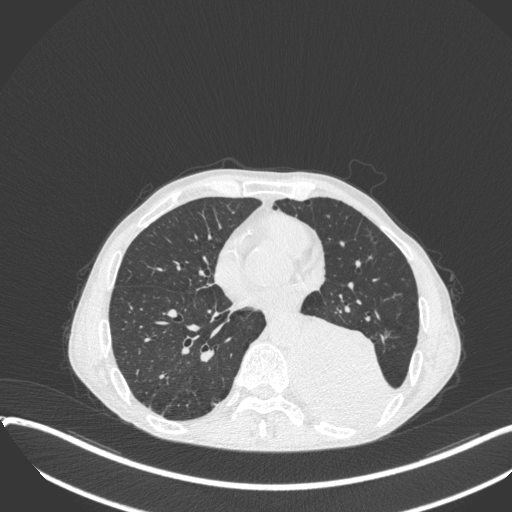
Chest CT, one axial slice. Slice 149 of 400 in the series (ordered by position). 120 kVp. Lung window (W 1500 / L -600 HU). 1 mm slice thickness. 512 × 512 image matrix, field of view 400 × 400 mm. Patient: male, 57 years. From the clinical record (not read from this slice): clinical TNM (as recorded): T4 N0 M0.
Structures marked on this image (bounding box drawn by a radiologist):
- lung tumour (recorded histology: squamous cell carcinoma): bounding box [x1, y1, x2, y2] px = [287, 307, 395, 436]